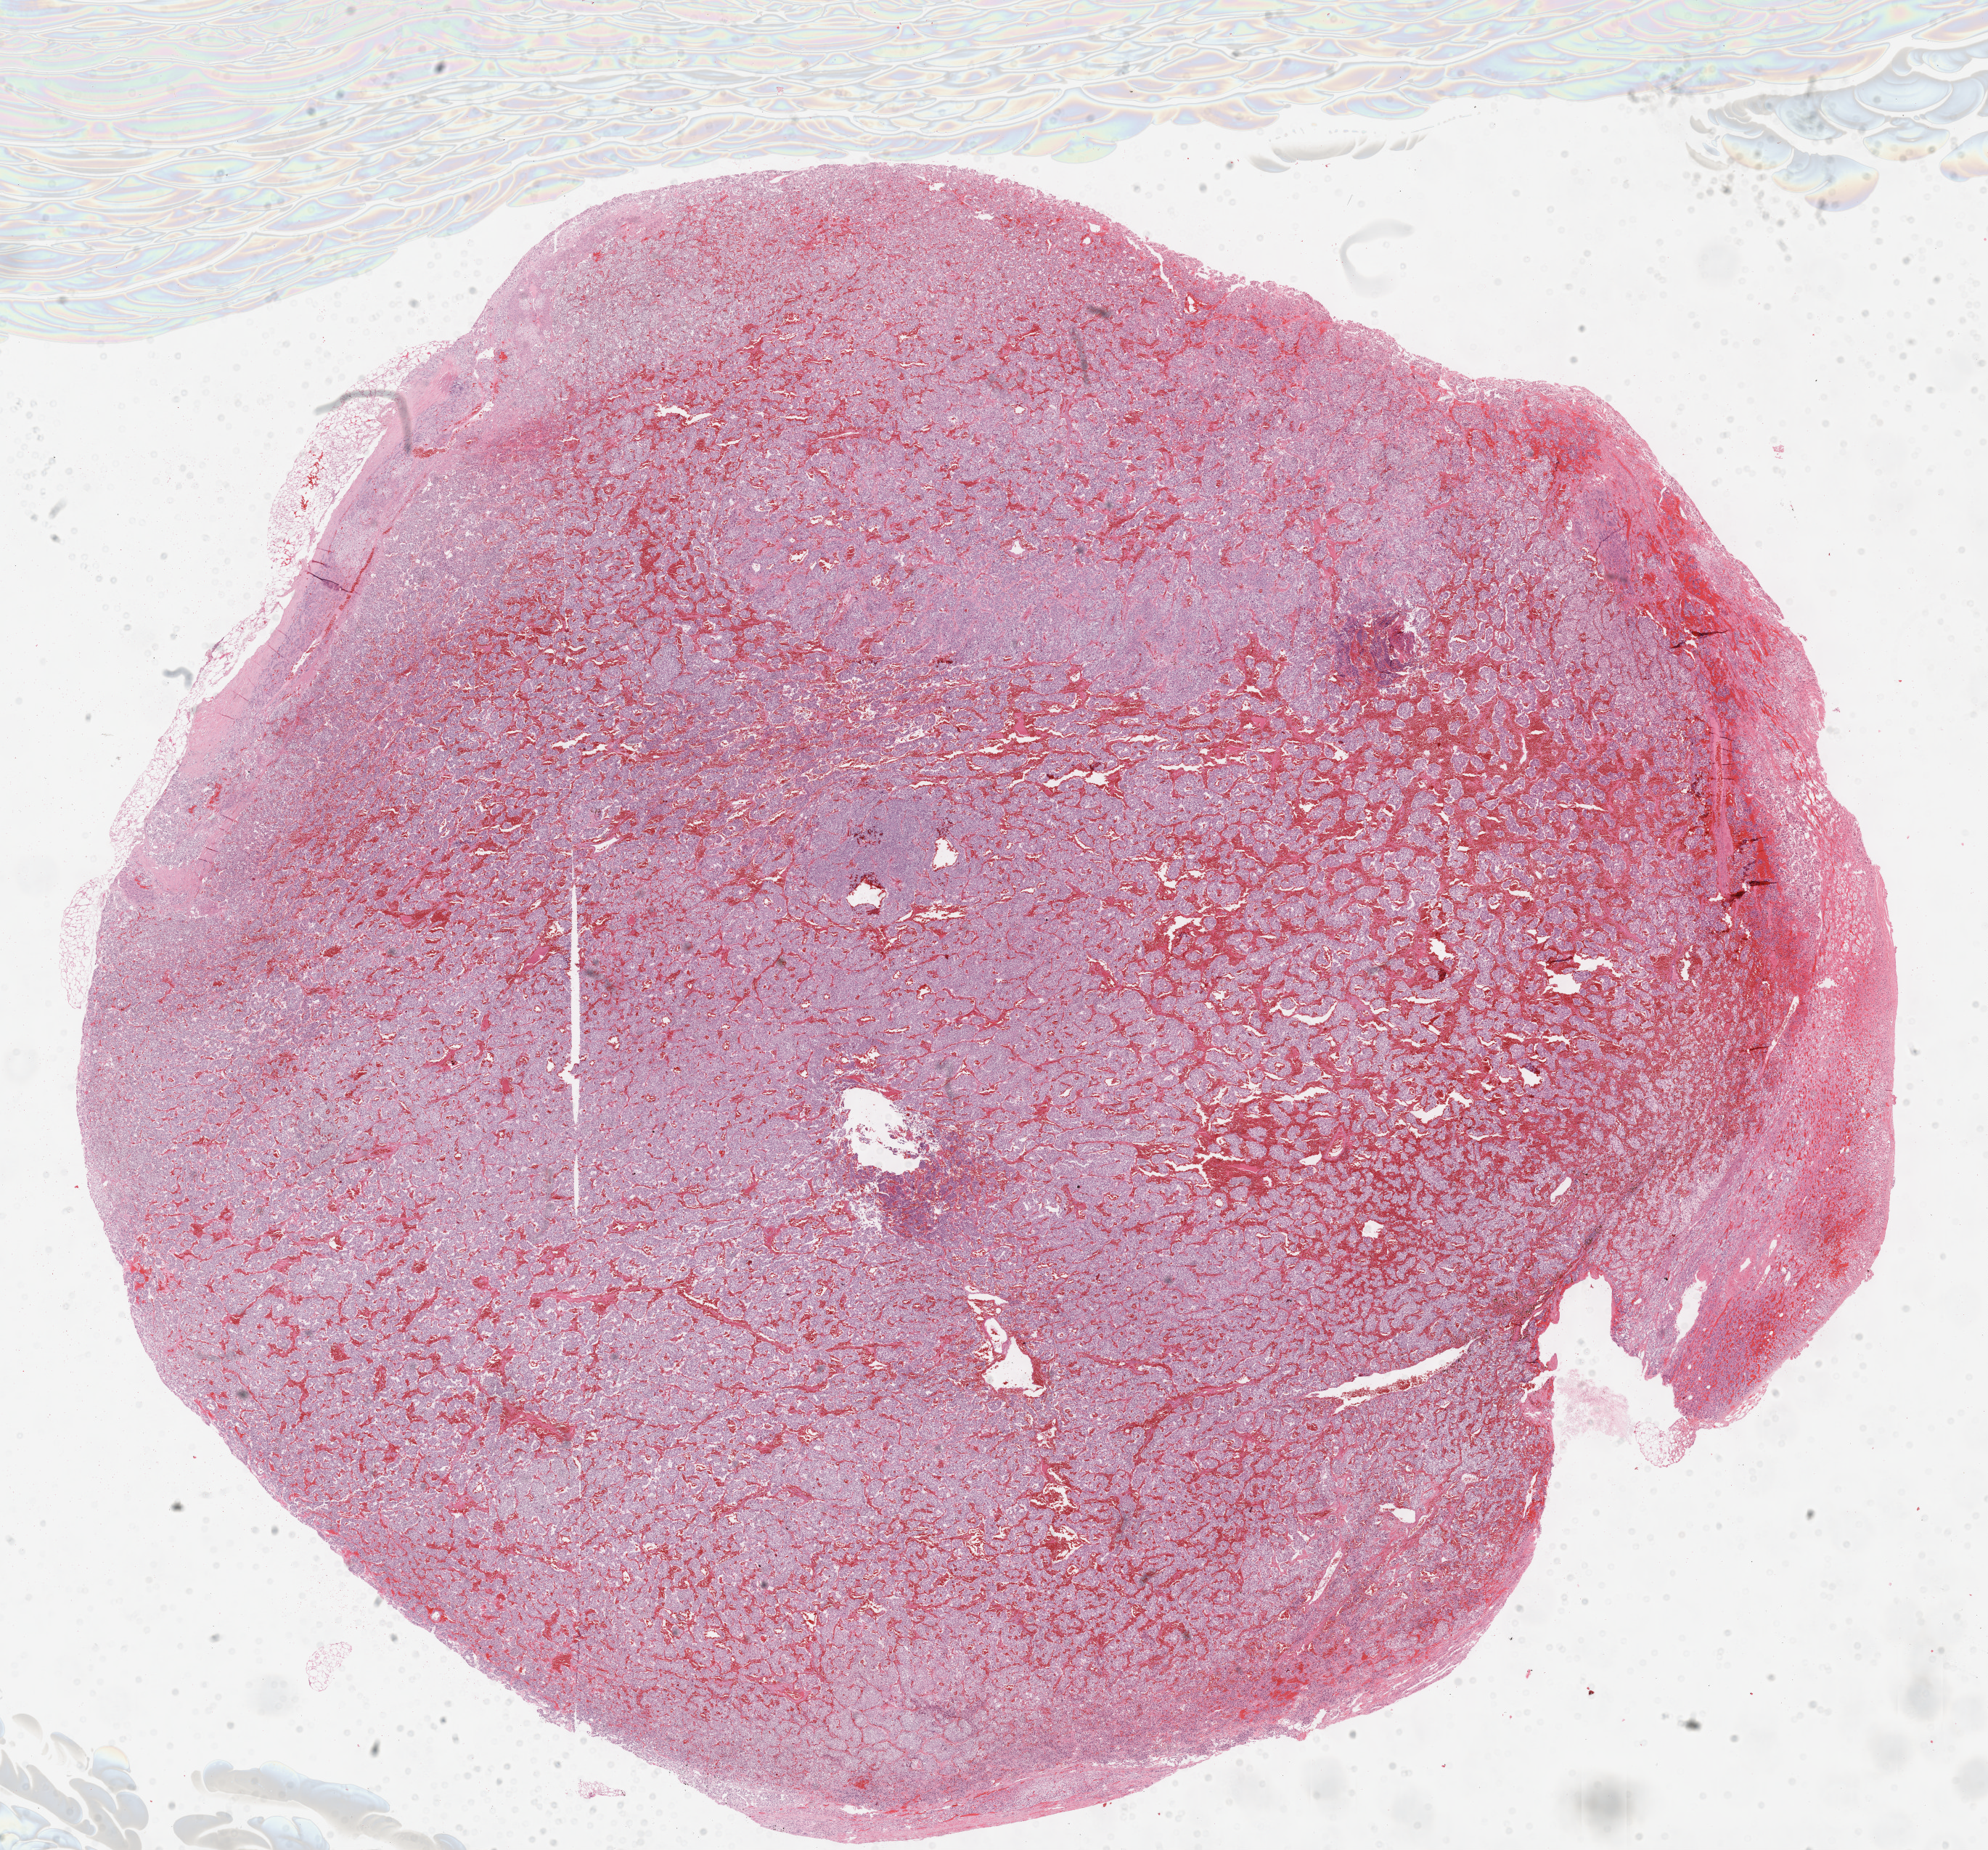
Whole-slide histology image, H&E-stained — a low-resolution overview of the entire scanned area, about 22.1 x 20.6 mm. FFPE section. Primary tumour sample from the adrenal gland. Patient: female, age at initial diagnosis 57 years.
Diagnosis: Pheochromocytoma, NOS (cortex of adrenal gland).